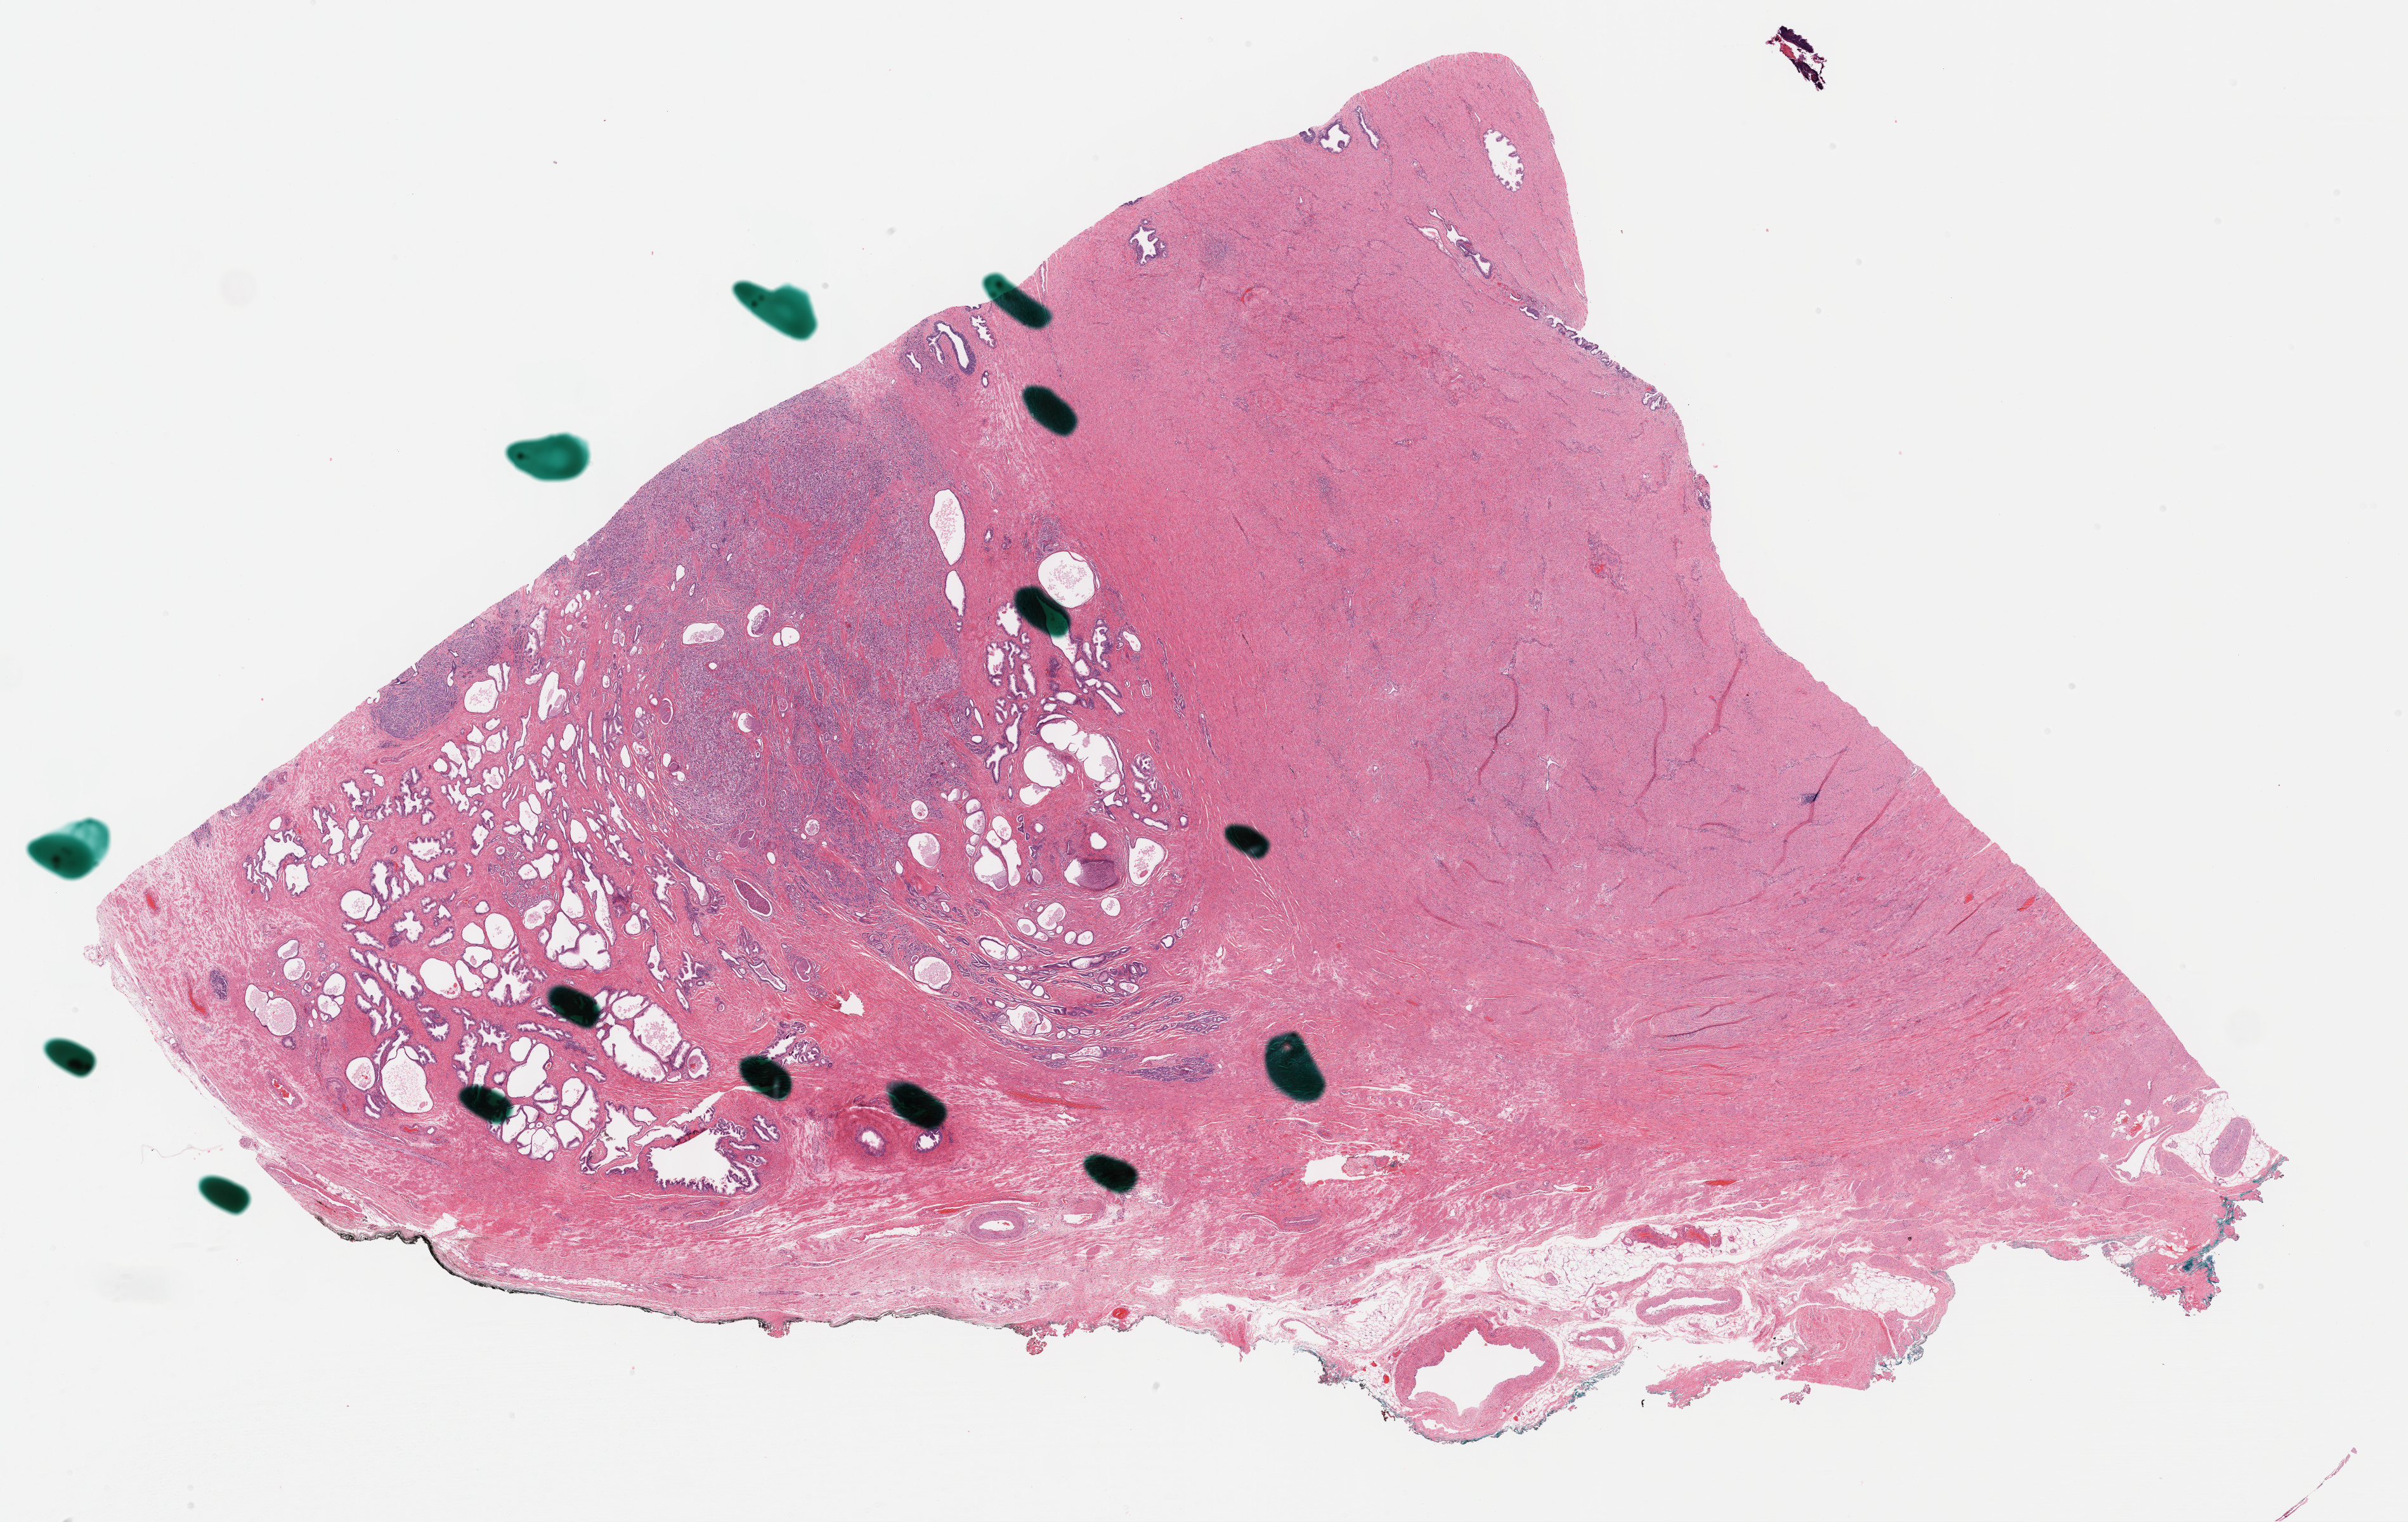
Hematoxylin and eosin (H&E) stained whole-slide image, shown as a low-resolution overview of the whole scanned area (about 30.7 x 19.4 mm, acquisition: 40x scan), formalin-fixed paraffin-embedded (FFPE) diagnostic section, prostate, primary tumour sample. Male, age 54 years at initial diagnosis. Gleason score: 9 (5+4).
Lymph nodes positive (case pathology): 0 of 10 examined. Pathologic diagnosis: Adenocarcinoma, NOS.